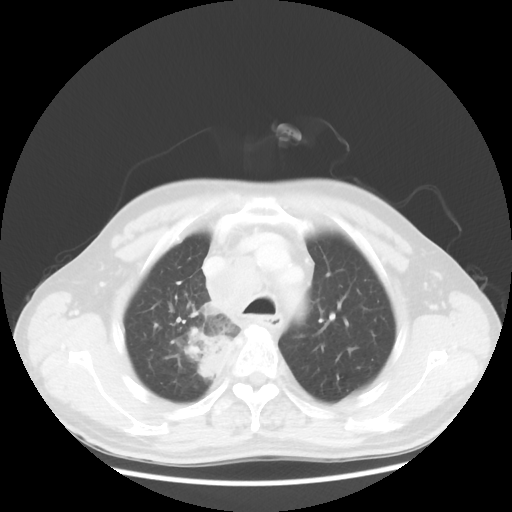
Chest CT, one axial slice. Slice 96 of 124 in the series (ordered by position). Lung window (W 1500 / L -600 HU). 5 mm slice thickness. 512 × 512 image matrix, field of view 382 × 382 mm. Male patient, age 64 years. From the clinical record (not read from this slice): clinical TNM (as recorded): T3 N3 M0.
Outlined on this slice (rectangle marked by the reading radiologist):
- lung tumour (recorded histology: small cell carcinoma): box from (x=184, y=298) to (x=248, y=392) px